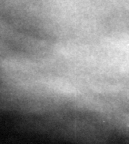
Crop from a digitized film mammogram around one marked abnormality, right breast, MLO view, BI-RADS breast density category 3 (scale 1–4).
Calcifications, morphology lucent center; BI-RADS assessment category 2; benign; no additional work-up was recommended (benign without callback).